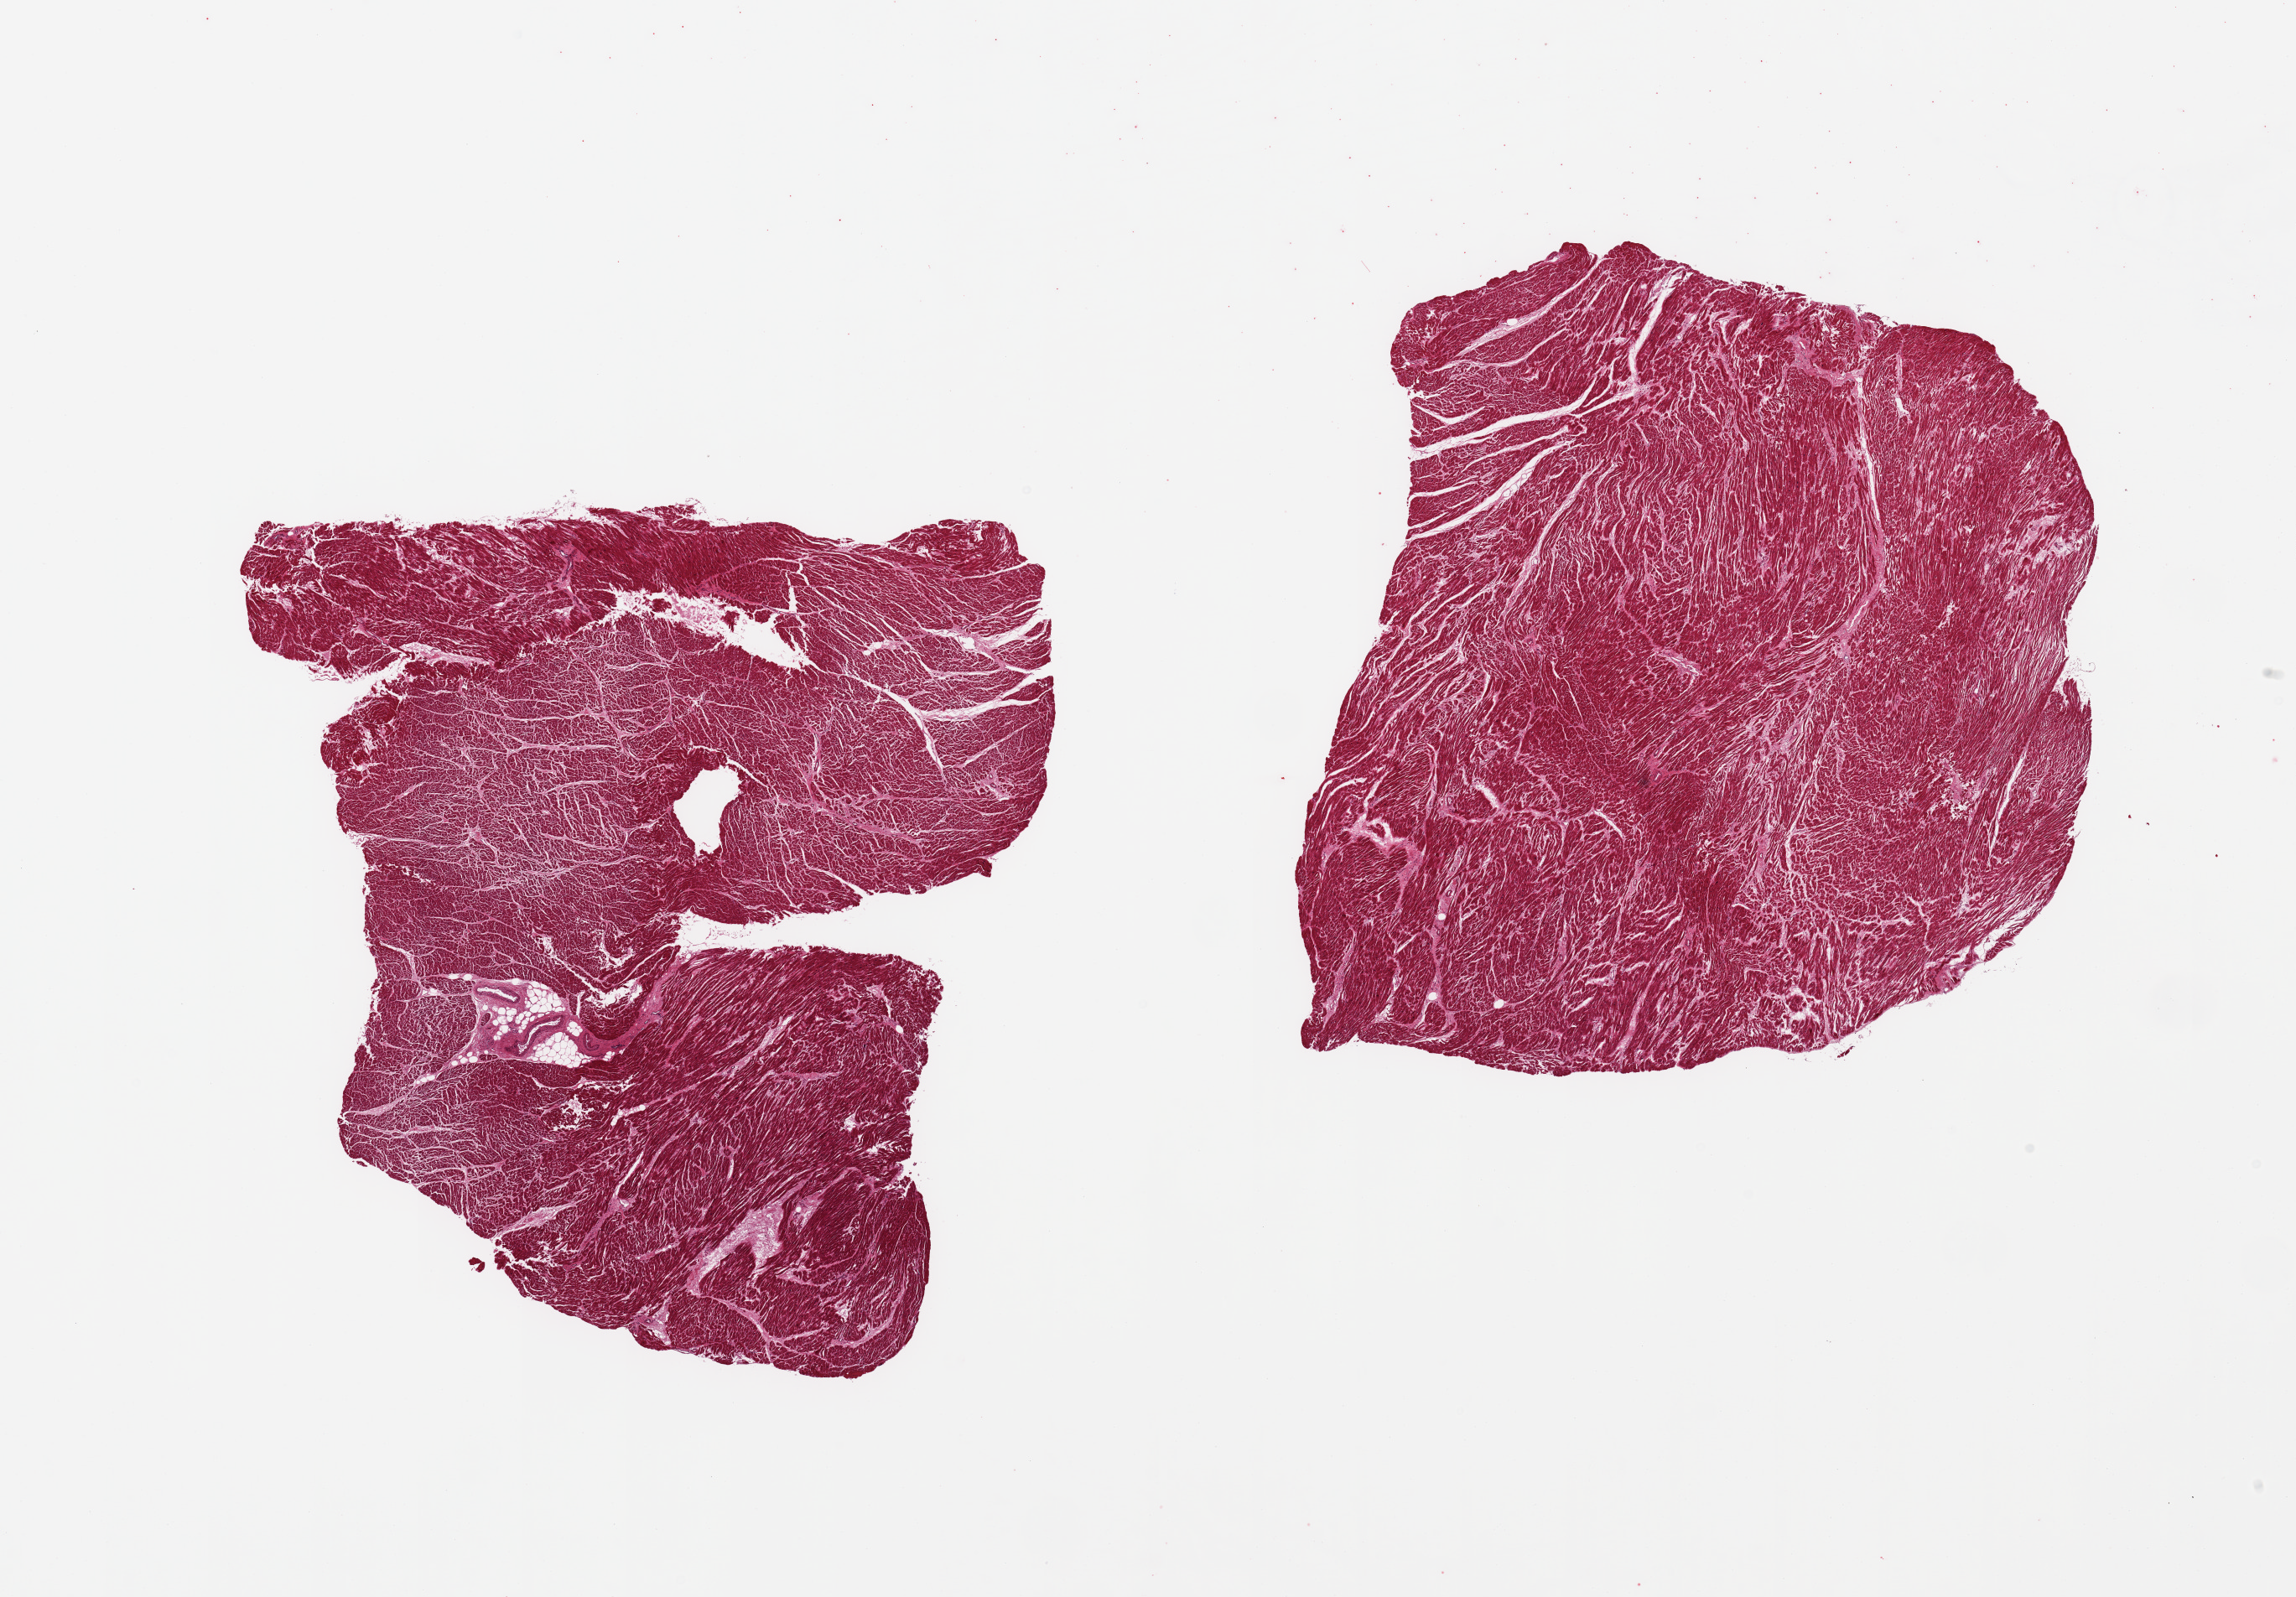
Whole-slide image, hematoxylin and eosin (H&E) stain — a low-resolution overview of the entire scanned area, about 21.7 x 15.1 mm, PAXgene-fixed paraffin-embedded (PFPE) section, section of heart (target tissue), tissue donor sample. Donor: male.
Pathologist's review note for this sample: 2 pieces; accentuation of interstitial connective tissue, patchy hypereosinophilia and fragmented fibers (?early ischemic change).